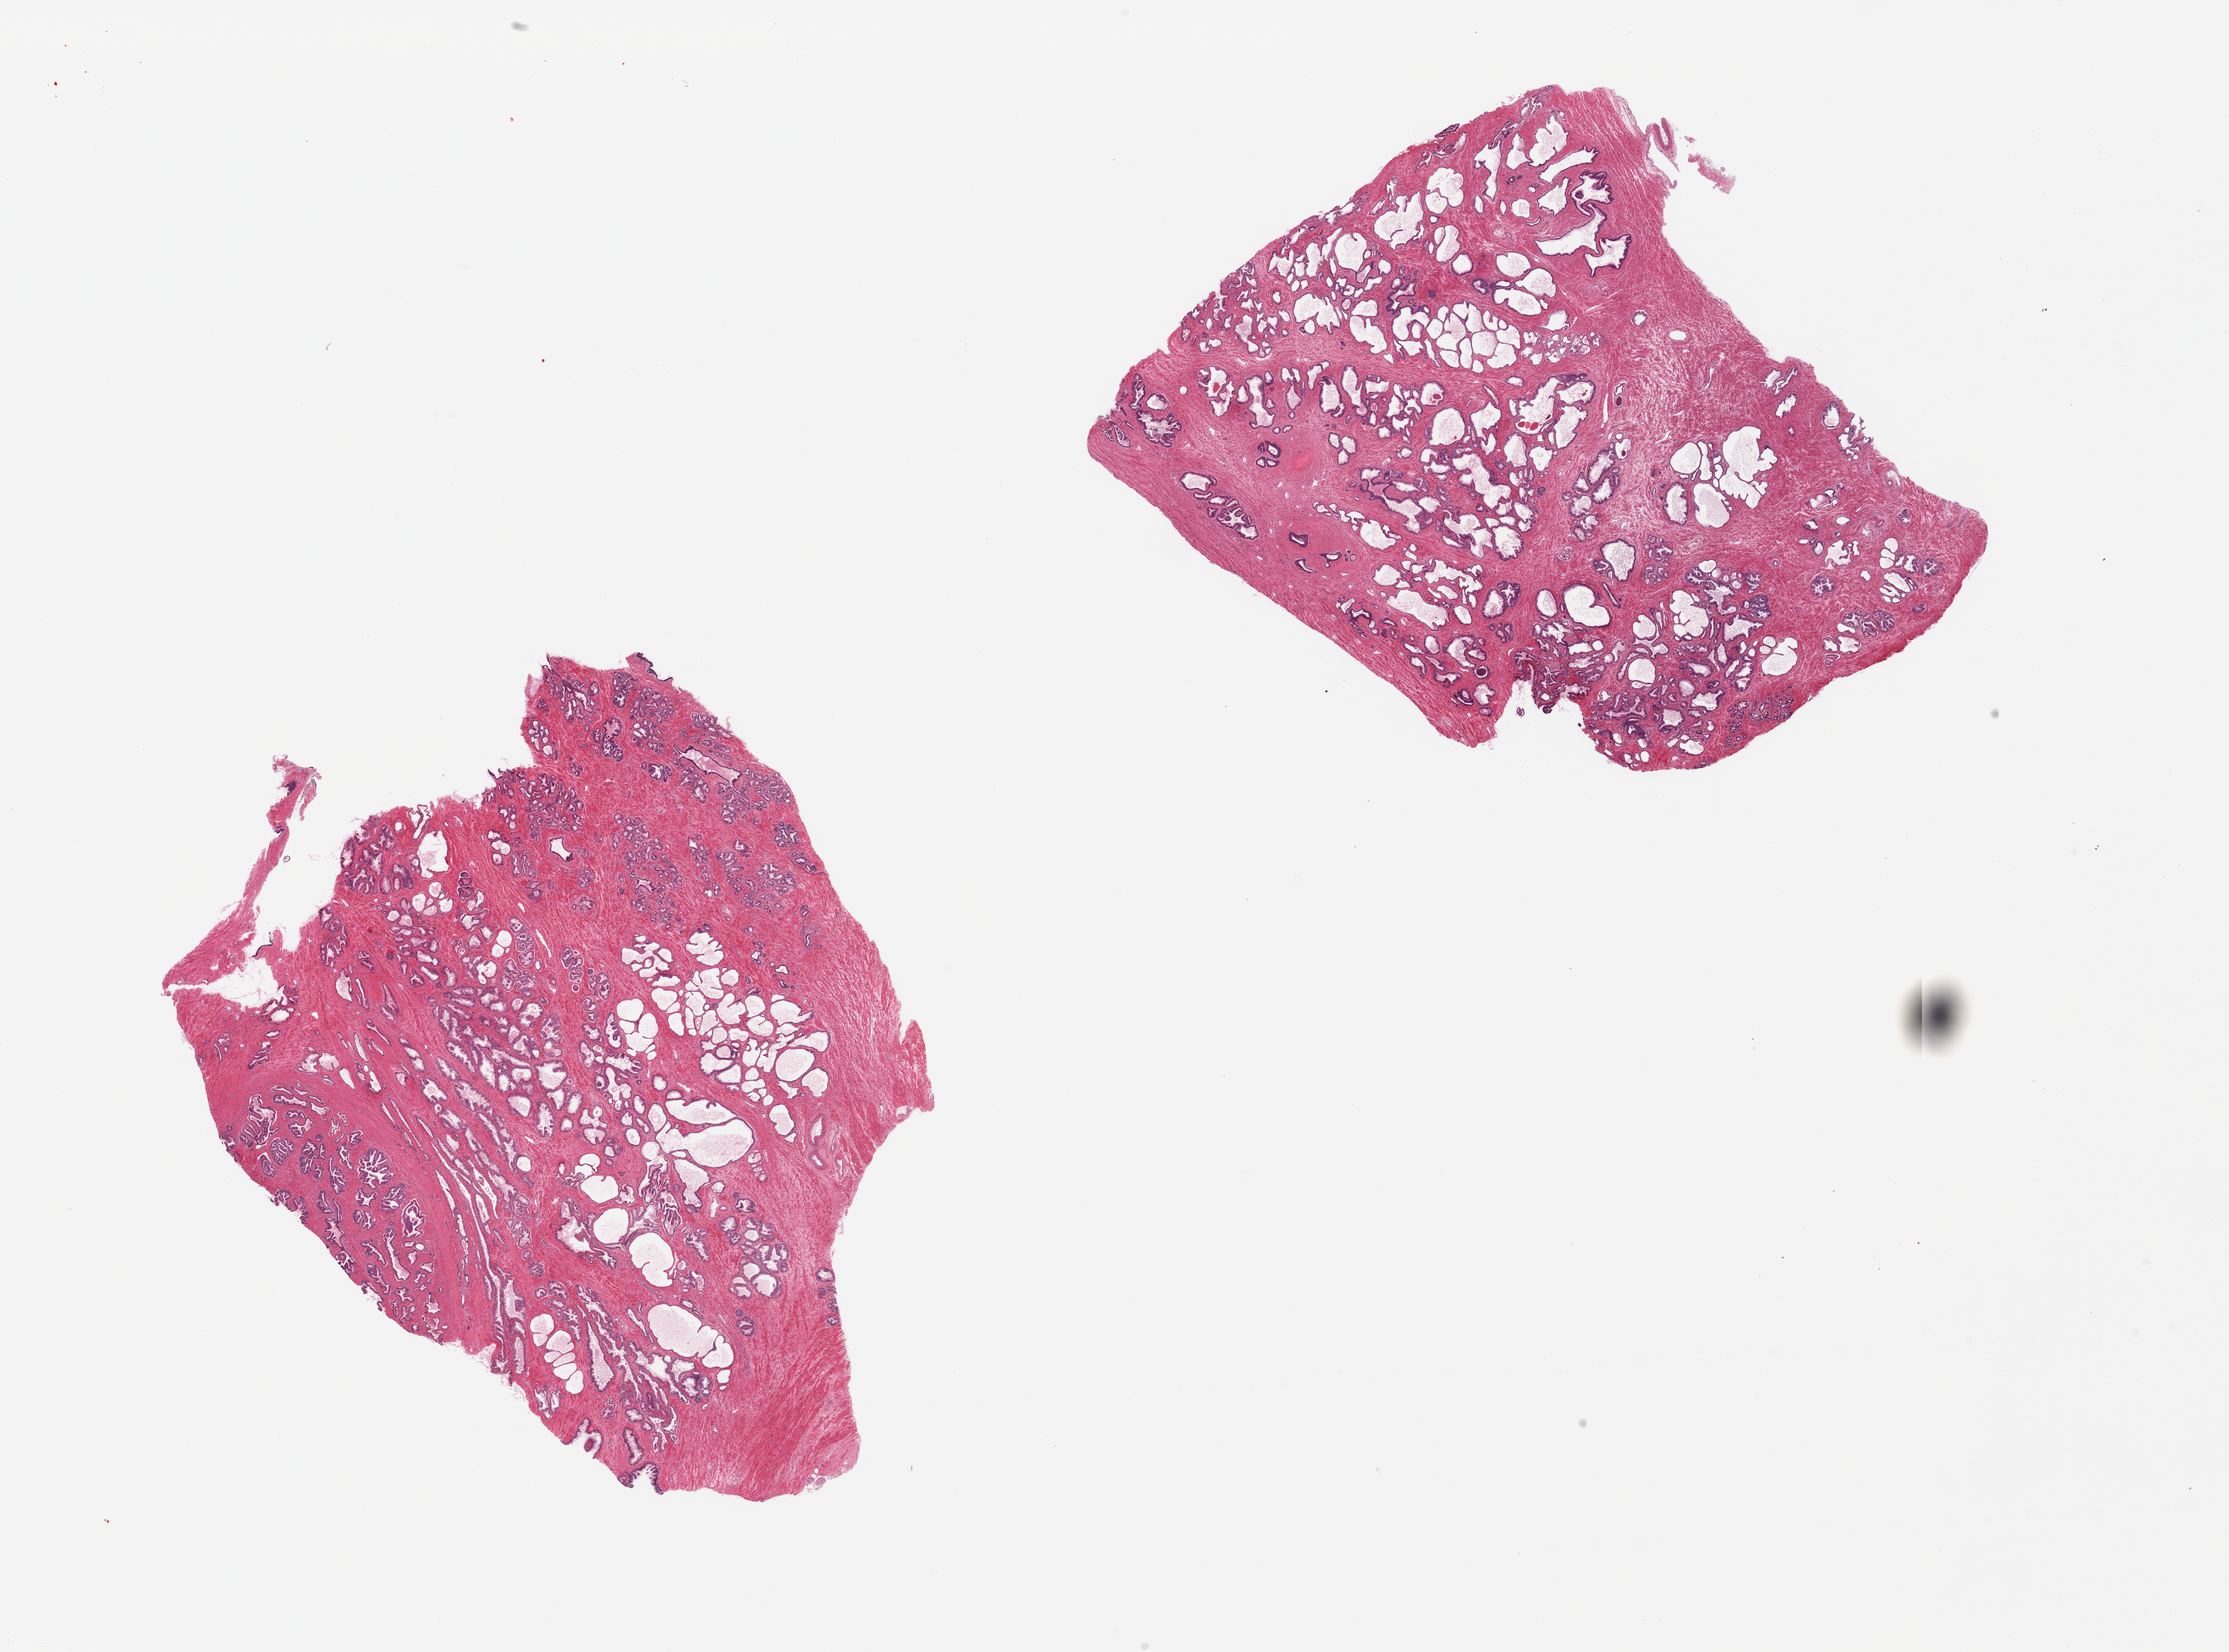
Whole-slide image, haematoxylin and eosin stain, a low-resolution overview of the entire scanned area, about 28.5 x 21.2 mm. PAXgene-fixed, paraffin-embedded tissue. Sampled site (target tissue): prostate. Donor tissue sample.
Reviewer comment on this tissue sample: 2 pieces. Autolysis varies from slight to moderate.